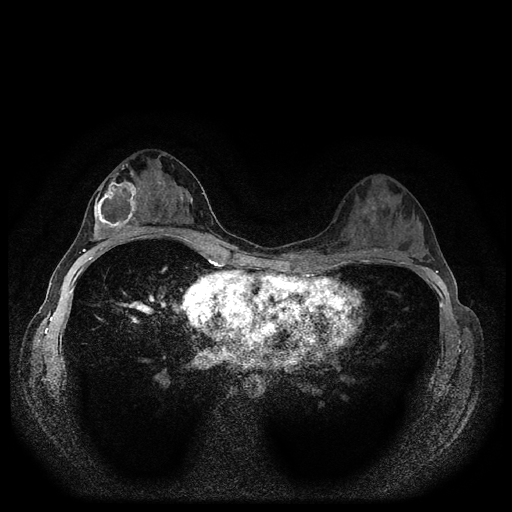
Breast MRI (dynamic contrast-enhanced, multi-phase), one axial slice. Slice 59 of 116 in the series (ordered by position). Dynamic contrast-enhanced series, time point 2 of 5 at this slice position (early post-contrast). 1.5 T. TE 2.7 ms, TR 5.4 ms. 2 mm slice thickness. 512 × 512 image matrix. Female patient, age 29 years.
Structures marked on this image (semi-automatic segmentation, software-assisted and operator-edited):
- breast lesion (labelled 'tumour' in the annotation; benign lesions carry a separate 'benign' label): bounding box [x1, y1, x2, y2] px = [89, 180, 141, 243]